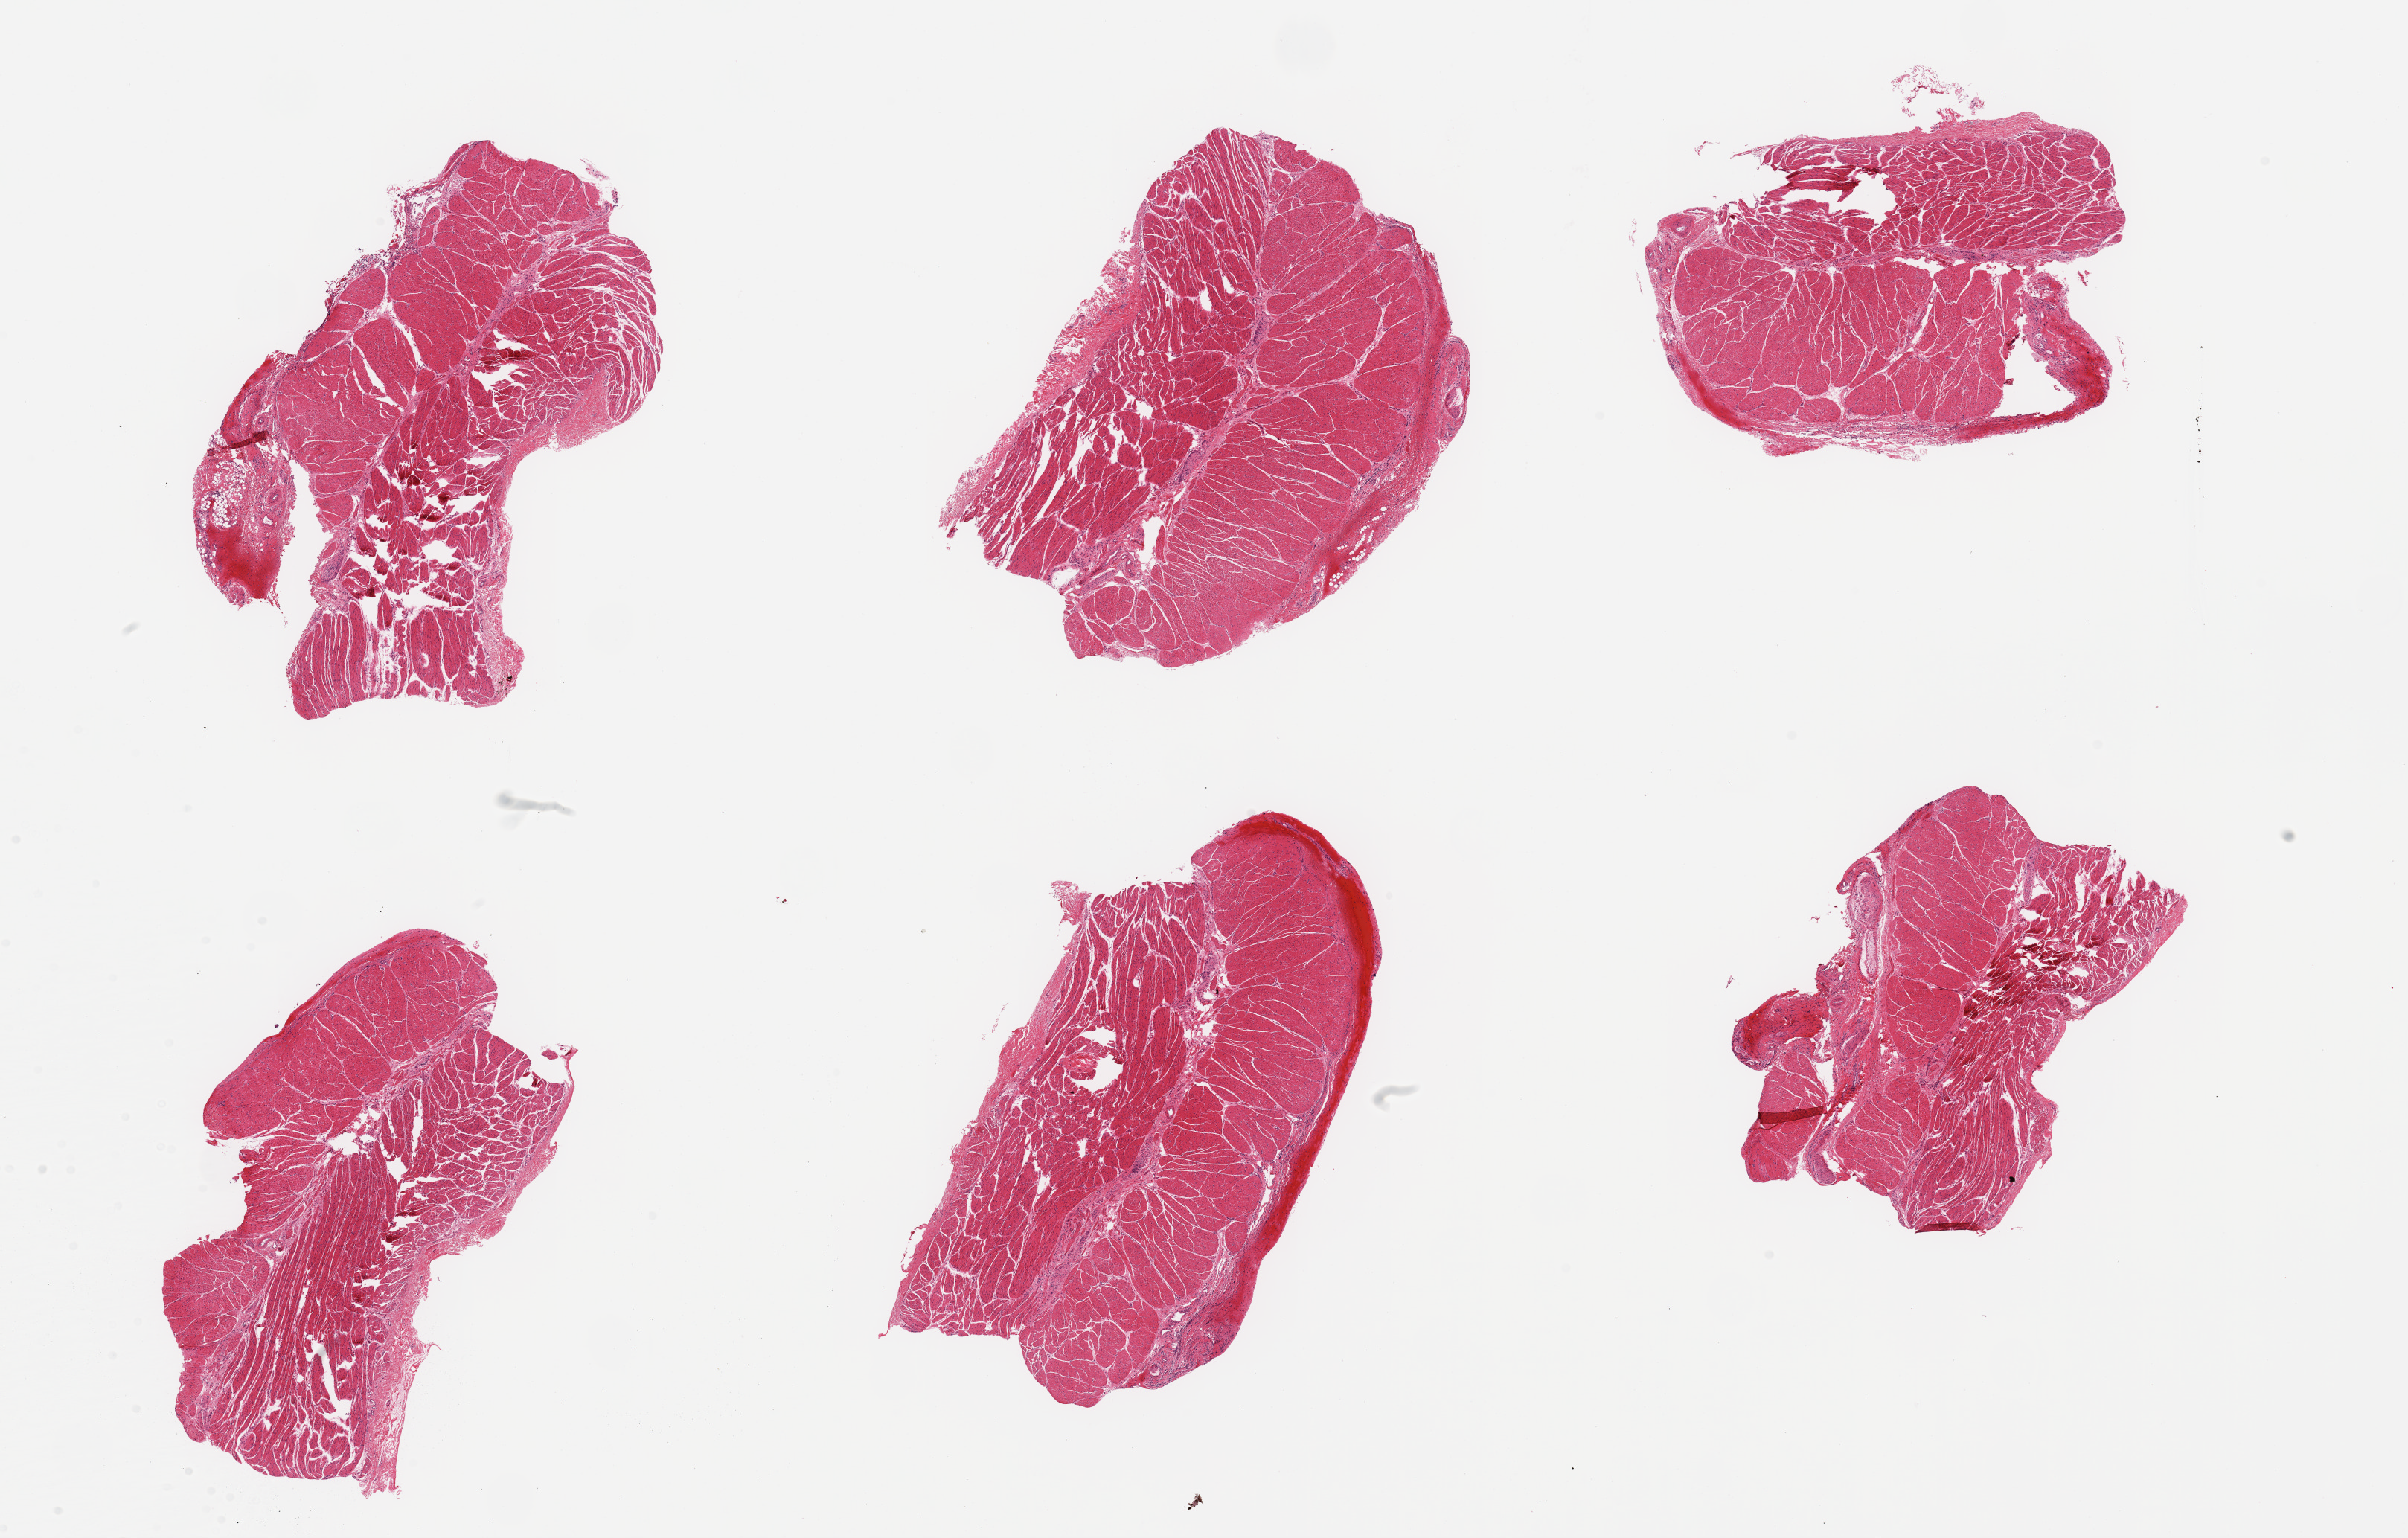
Haematoxylin and eosin whole-slide image, brightfield, low-resolution overview of the scanned area, about 25.6 x 16.3 mm (from a 20x scan). PAXgene-fixed paraffin-embedded (PFPE) section. Target tissue: esophageal muscle. Donor tissue sample. Donor sex: male.
Review note (as recorded): 6 pieces; target muscularis with focal acute inflammation and hemorrhage within adventitia.